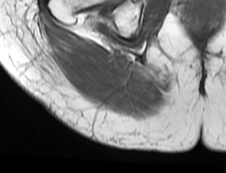
MRI of an extremity soft-tissue mass, one axial slice; position 22 of 73 along the scan axis; MR volume resampled by the dataset authors to the PET/CT grid (not the native acquisition matrix); 3.27 mm slice thickness; 226 × 173 image matrix, field of view 221 × 169 mm. Female patient. From the clinical record (not read from this slice): histological type: spindle cell suggestive of myxofibrosarcoma; grade: intermediate; site of the primary tumour: right buttock.
Outlined on this slice (expert contour drawn on MRI and transferred to this co-registered scan by the dataset authors):
- gross tumour volume (mass): box from (x=52, y=42) to (x=106, y=89) px